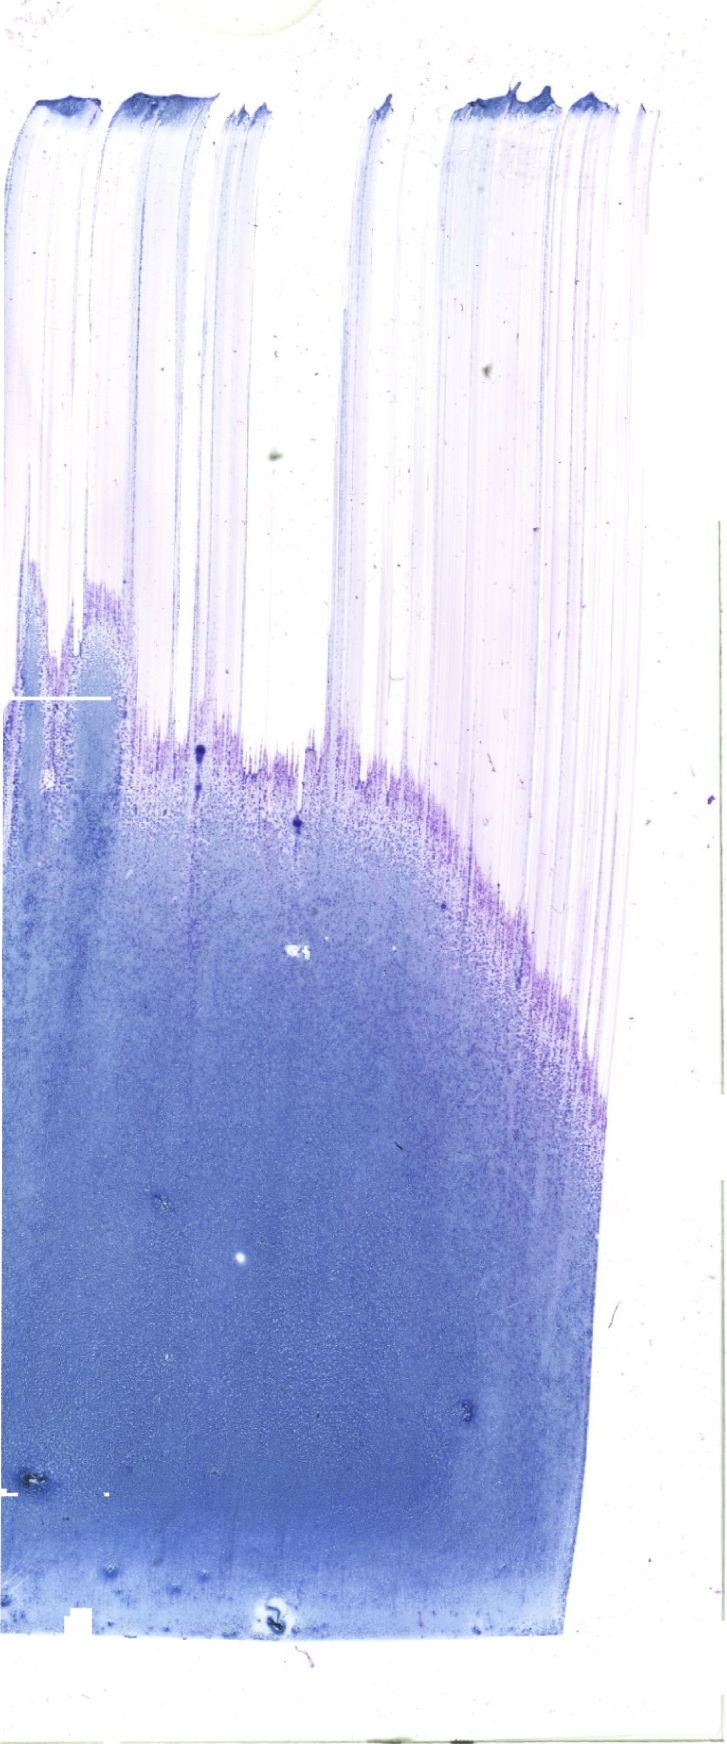
Bone marrow aspirate smear, May-Grünwald-Giemsa (MGG) stain, whole-slide image, whole scanned area (about 20.6 x 49.4 mm) shown as a low-resolution overview. Female patient.
Diagnosis: Acute Myeloid Leukemia with Maturation.